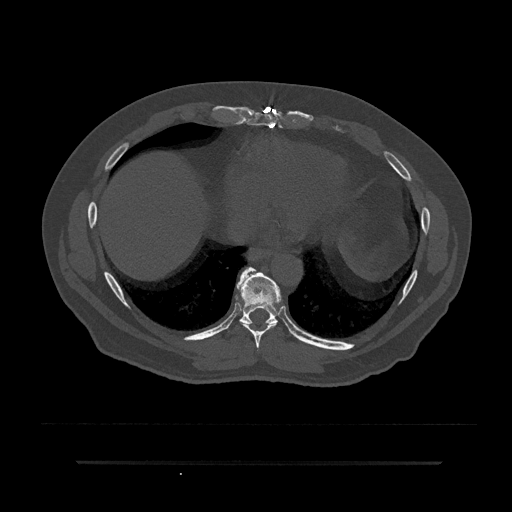
CT including the spine, one axial slice. Bone window (W 1800 / L 400 HU). 0.5 mm slice thickness. 512 × 512 image matrix, field of view 464 × 464 mm. Patient: male, 59 years. Case-level facts recorded for this patient, not image findings: primary cancer: bile ducts; vertebrae with lytic lesions (as recorded): T10.
Annotated regions visible in this slice (semi-automatically segmented with operator editing):
- T8 vertebra: bounding box [x1, y1, x2, y2] px = [242, 323, 276, 350]
- T9 vertebra: [227, 267, 281, 329]